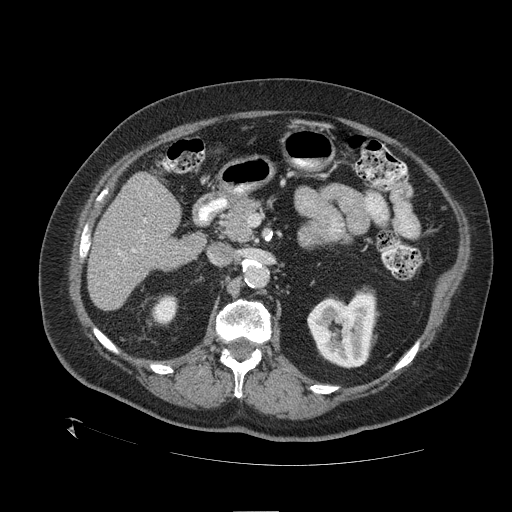
Contrast-enhanced abdominal CT (liver protocol), one axial slice; slice 56 of 109 in the series (ordered by position); one of 2 acquisitions stored at this slice position; soft-tissue window (W 400 / L 40 HU); 2.5 mm slice thickness; 512 × 512 image matrix. Case-level facts recorded for this patient, not image findings: diagnosis: hepatocellular carcinoma (patient treated with transarterial chemoembolisation; whether this scan precedes or follows treatment is not stated here); TNM stage (as recorded): Stage-I; Child-Pugh class: A; tumour differentiation: no biopsy; tumour size: 4.6 cm.
Annotated regions visible in this slice (semi-automatically segmented with operator editing):
- liver parenchyma outside the tumour (the mass and vessels are separate outlines, so this box may not span the whole liver): bounding box (x1, y1, x2, y2) in pixels: (88, 172, 204, 310)
- liver vessels: (117, 219, 146, 253)